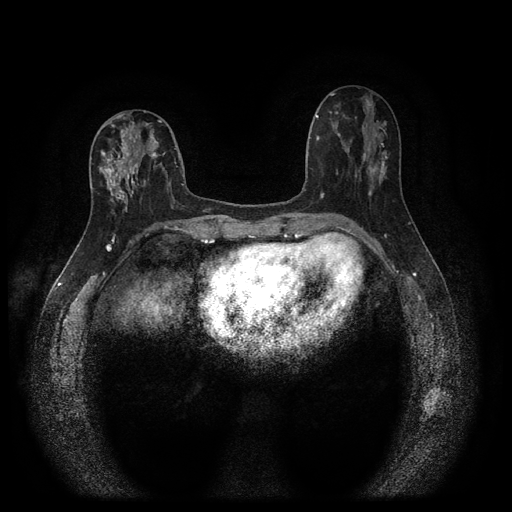
Breast MRI (dynamic contrast-enhanced, multi-phase), one axial slice. Slice 43 of 116 in the series (ordered by position). Dynamic contrast-enhanced series, time point 2 of 5 at this slice position (early post-contrast). 1.5 T. TE 2.7 ms, TR 5.4 ms. 512 × 512 image matrix, field of view 330 × 330 mm. Female patient, age 47 years.
Outlined on this slice (semi-automatically segmented with operator editing):
- breast lesion (labelled 'tumour' in the annotation; benign lesions carry a separate 'benign' label): bounding box <99,121,161,211> (left, top, right, bottom; pixels)